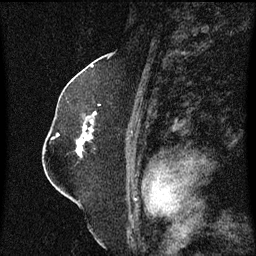
Breast MRI (dynamic contrast-enhanced), one sagittal slice. Slice 38 of 60 in the series (ordered by position). Dynamic contrast-enhanced series, image 2 of 3 at this slice position (ordered by acquisition). 1.5 T. TE 4.2 ms, TR 8.4 ms. 2 mm slice thickness. 256 × 256 image matrix, field of view 200 × 200 mm. Patient: female, 52 years. From the clinical record (not read from this slice): setting: breast cancer imaged before/during neoadjuvant chemotherapy; receptor status: HR-positive, HER2-negative.
Annotated regions visible in this slice (semi-automatic segmentation, software-assisted and operator-edited):
- analysis volume of interest (the breast-tissue region the enhancement analysis was run in; not a lesion): bounding box <77,104,101,159> (left, top, right, bottom; pixels)
- tumour enhancement mask (voxels above the 70 % enhancement threshold inside the analysis volume of interest): <77,114,97,157>